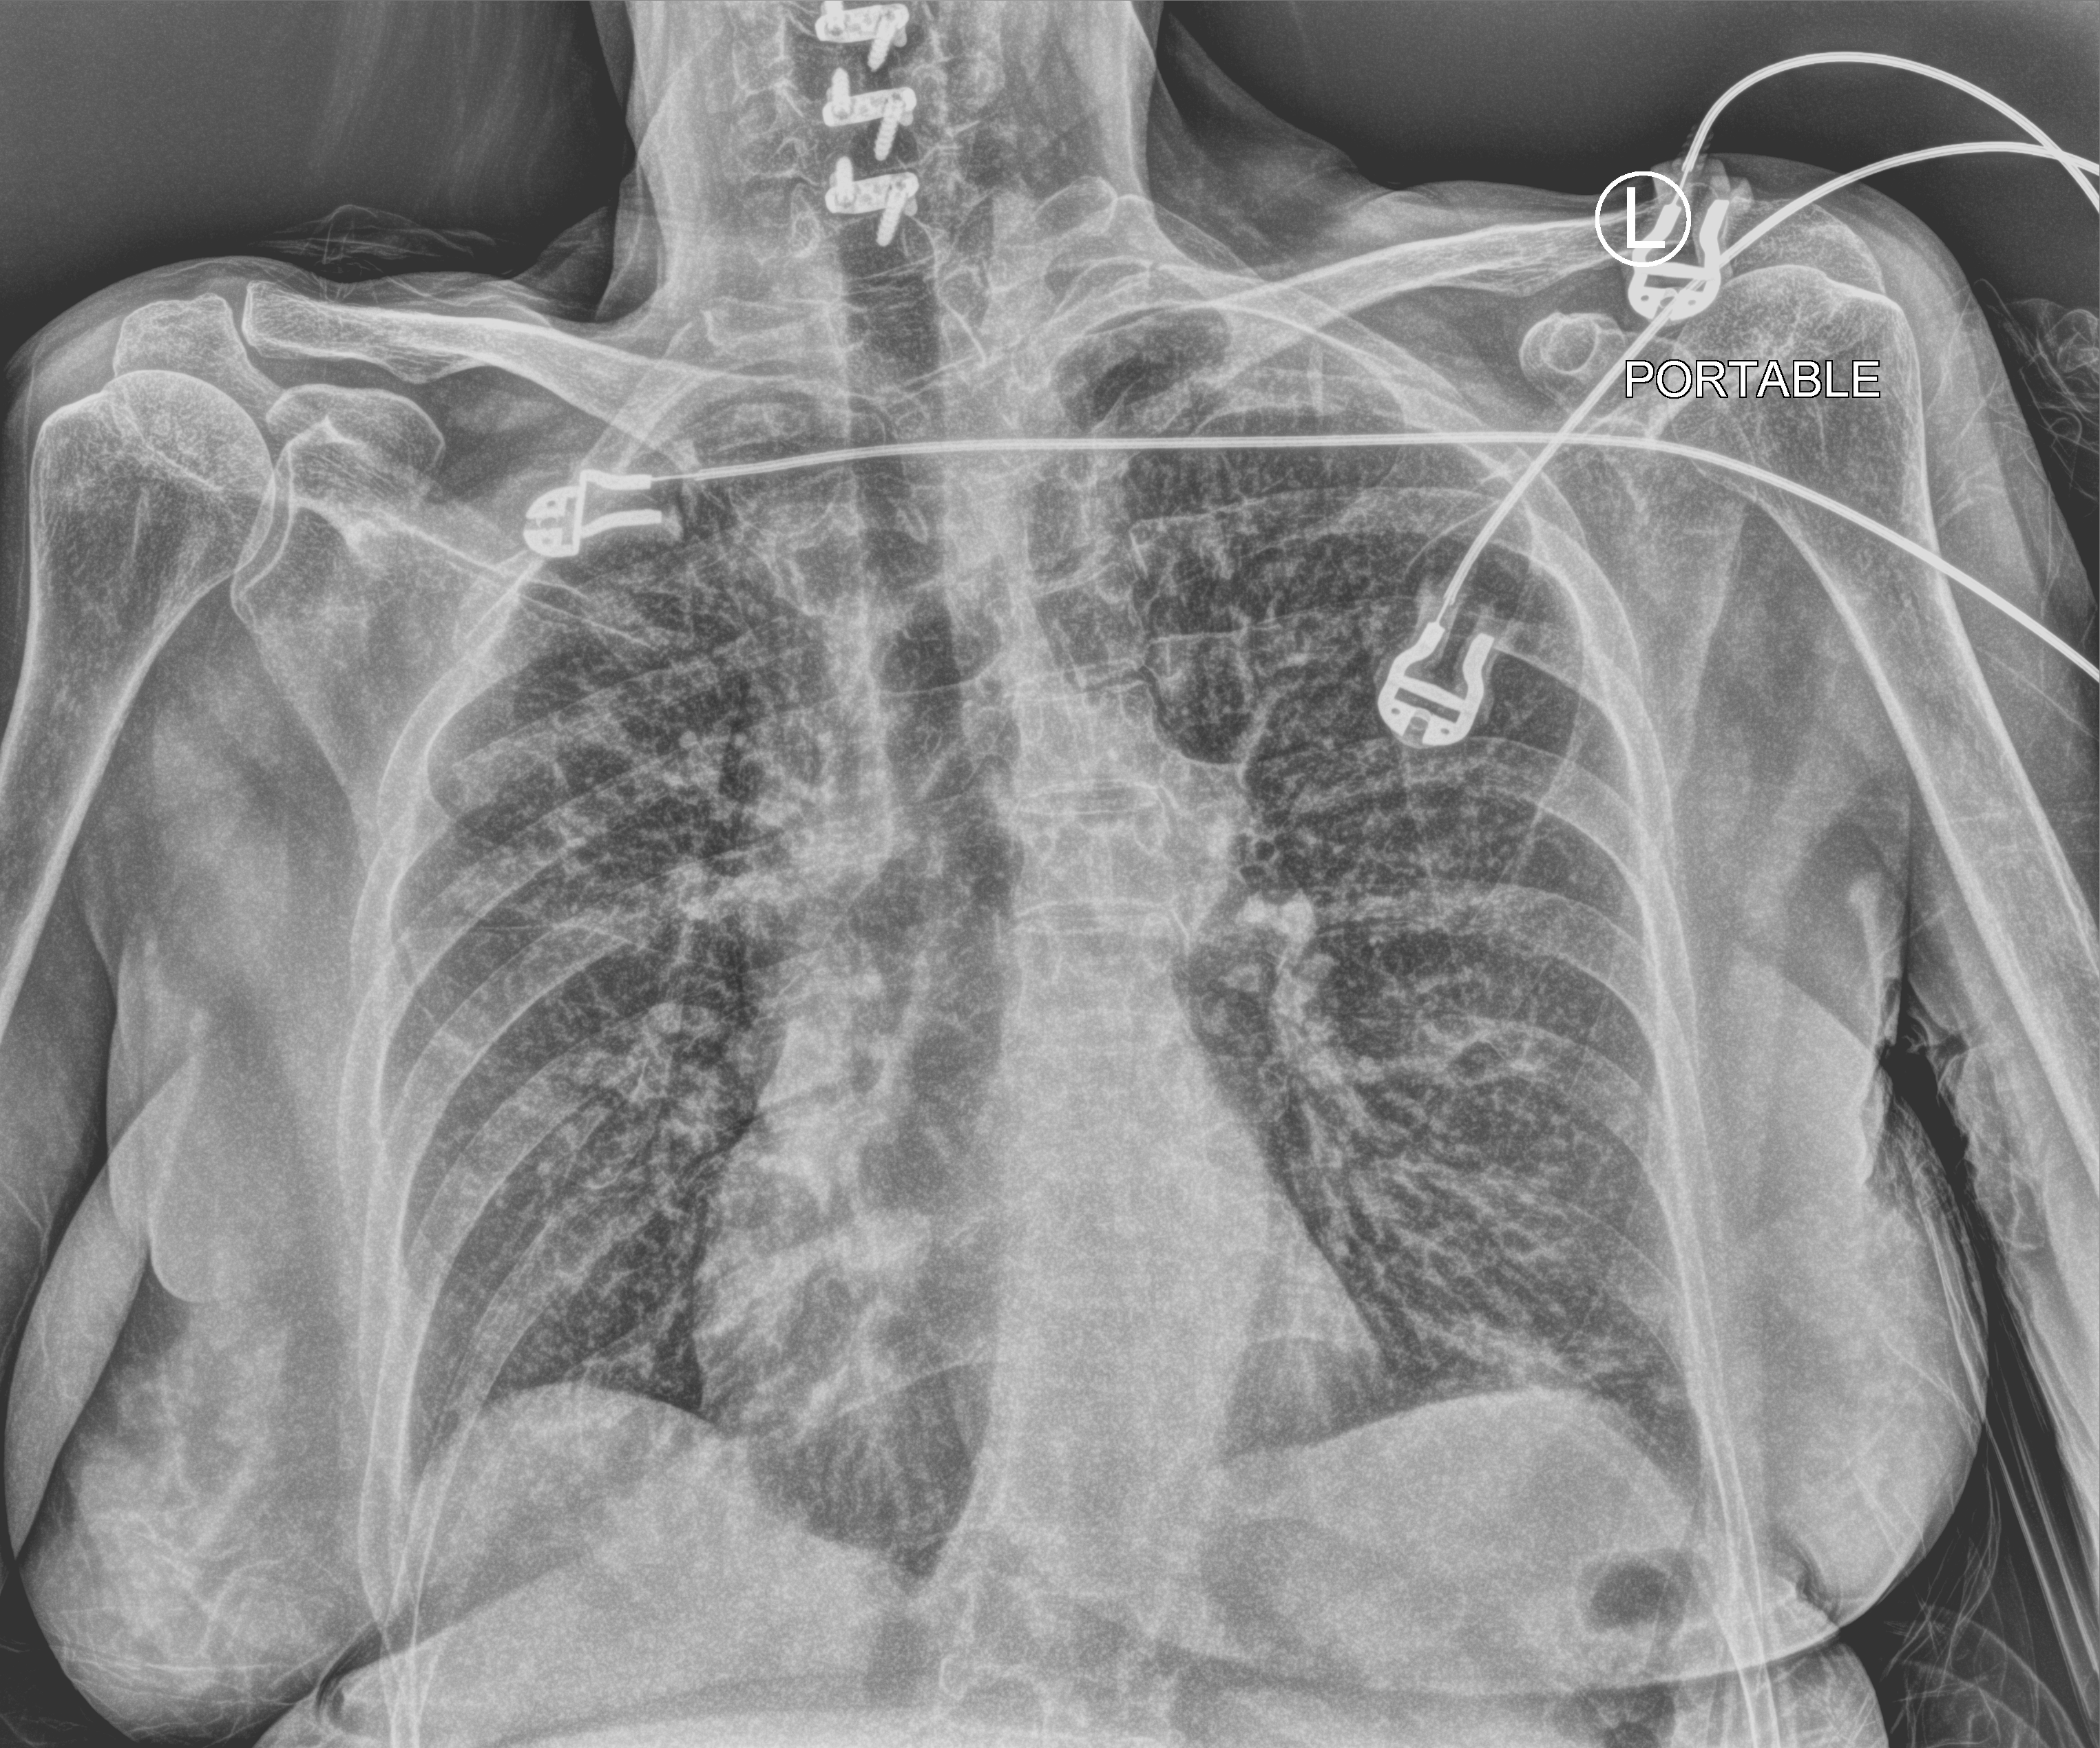
Bedside chest radiograph (computed radiography); anteroposterior (AP) projection. Female patient hospitalised with COVID-19, age 60–74 years.
Admission-level facts for this patient (not findings on this image; timing relative to this image not recorded): admitted to intensive care during this hospital stay: no.